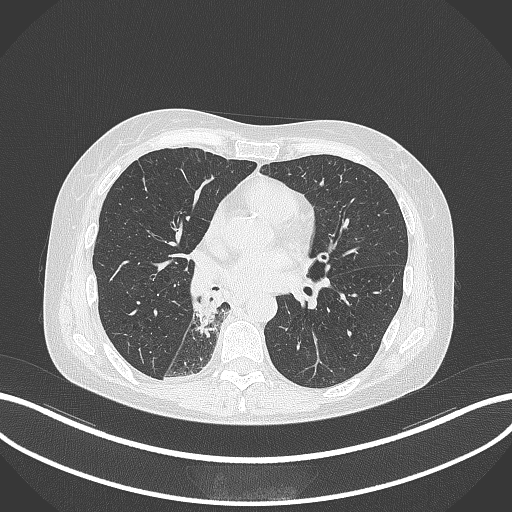
Chest CT, one axial slice; position 147 of 329 along the scan axis; 120 kVp; lung window (W 1500 / L -600 HU); 512 × 512 image matrix, field of view 400 × 400 mm. Female patient, age 63 years. Case-level facts recorded for this patient, not image findings: clinical TNM (as recorded): T1c N0 M0.
Annotated regions visible in this slice (rectangle marked by the reading radiologist):
- lung tumour (recorded histology: adenocarcinoma): bounding box (x1, y1, x2, y2) in pixels: (194, 289, 218, 336)